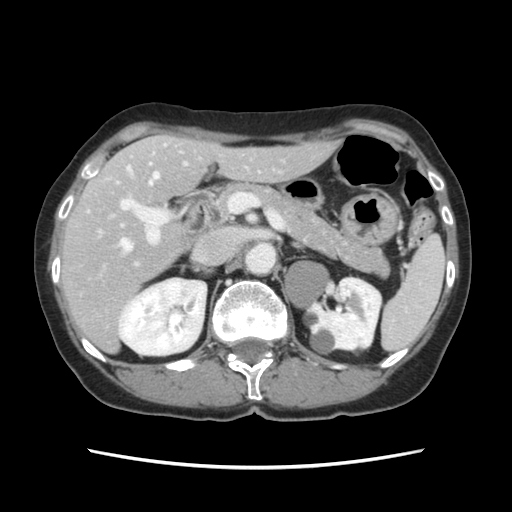
Contrast-enhanced abdominal CT, one axial slice; slice 71 of 120 in the series (ordered by position); intravenous contrast given; soft-tissue window (W 400 / L 40 HU); 2.5 mm slice thickness; 512 × 512 image matrix. Female patient, age 70 years. From the clinical record (not read from this slice): diagnosis: colorectal cancer liver metastases, imaged before liver resection; multiple liver metastases: no; largest metastasis: 2.5 cm; disease in both lobes: no.
Outlined on this slice (manually delineated by an expert):
- hepatic veins: bounding box [x1, y1, x2, y2] px = [120, 173, 159, 251]
- liver: [62, 136, 336, 350]
- planned liver remnant (the part of the liver to remain after resection): [88, 136, 336, 279]
- portal vein (with intrahepatic branches): [112, 145, 232, 265]